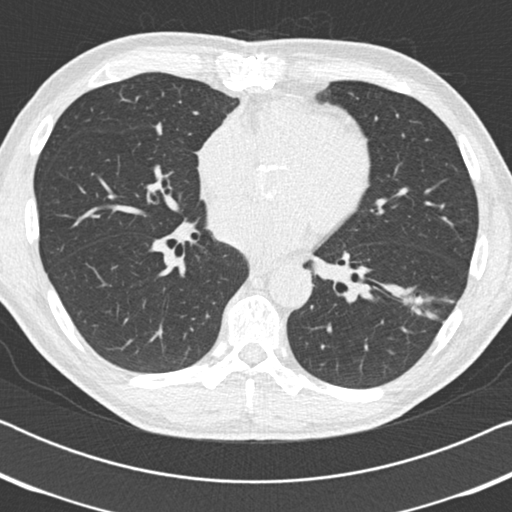
Chest CT (low-dose screening protocol), one axial image; third screening round (two years after baseline); lung window (W 1500 / L -600 HU); slice 104 of 186 in the series. Male participant, aged 59 years at enrolment. Current smoker at enrolment.
Lesion marked by an expert reader, bounding box [x1, y1, x2, y2] px = [387, 271, 456, 334]. The screening reader recorded 2 non-calcified nodules or masses ≥4 mm on this exam; which of them this box marks is not recorded. Lung cancer was diagnosed 73 days after this screen: adenocarcinoma, NOS, left lower lobe, poorly differentiated (G3), stage IA (AJCC 6th edition), 20 mm at pathology.